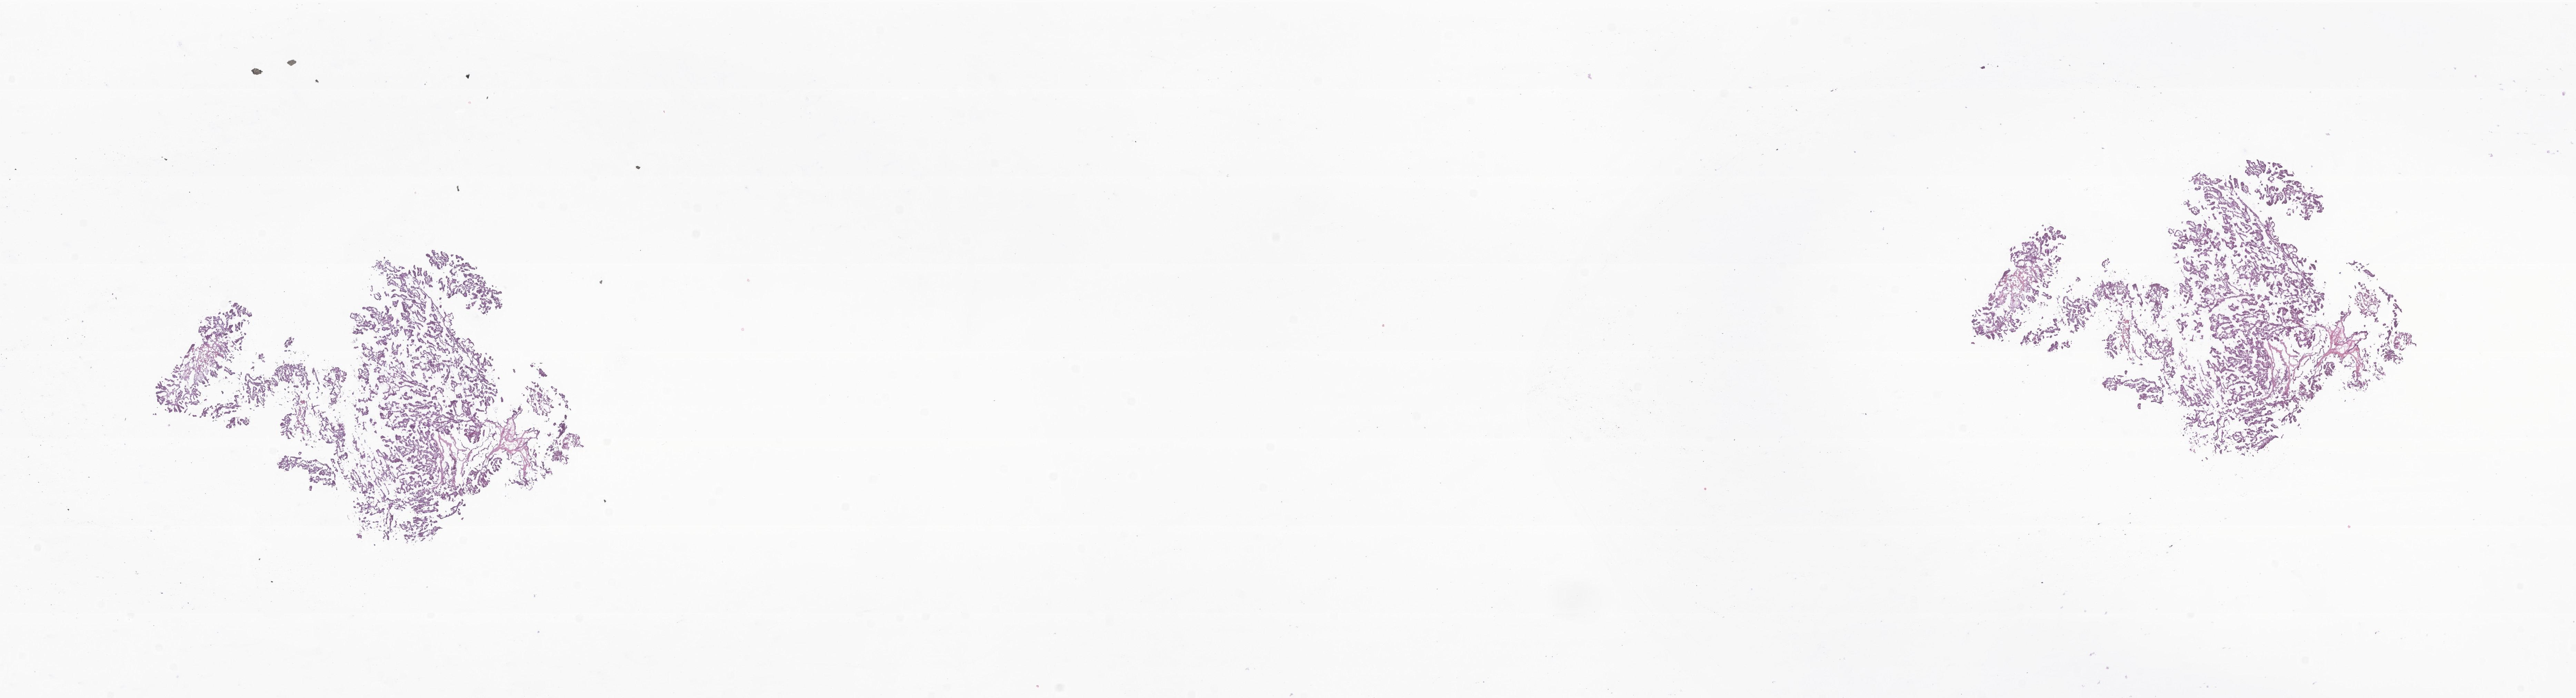
Whole-slide image, haematoxylin and eosin stain of tumor tissue from the brain — a low-resolution overview of the entire scanned area, about 31.5 x 8.5 mm. Frozen section. Patient: male, age 908 days (about 2.5 years).
Recorded diagnosis: Choroid plexus papilloma, NOS.